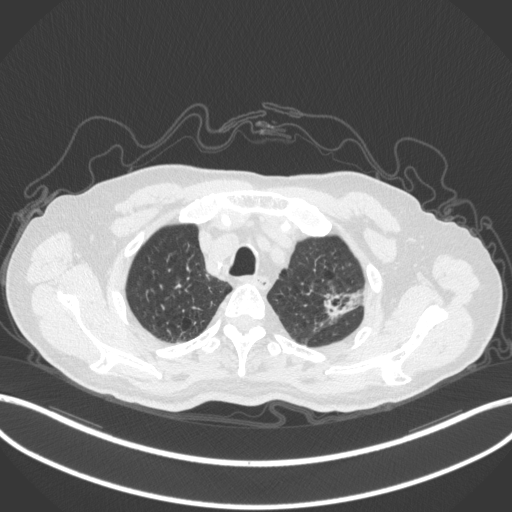
Chest CT, one axial slice. Slice 255 of 331 in the series (ordered by position). Reconstruction kernel B31f. 120 kVp. Lung window (W 1500 / L -600 HU). 512 × 512 image matrix, field of view 400 × 400 mm. Male patient, age 79 years. Case-level facts recorded for this patient, not image findings: clinical TNM (as recorded): T2a N1 M1; histopathological grade: G3.
Outlined on this slice (bounding box drawn by a radiologist):
- lung tumour (recorded histology: adenocarcinoma): box from (x=322, y=284) to (x=374, y=322) px